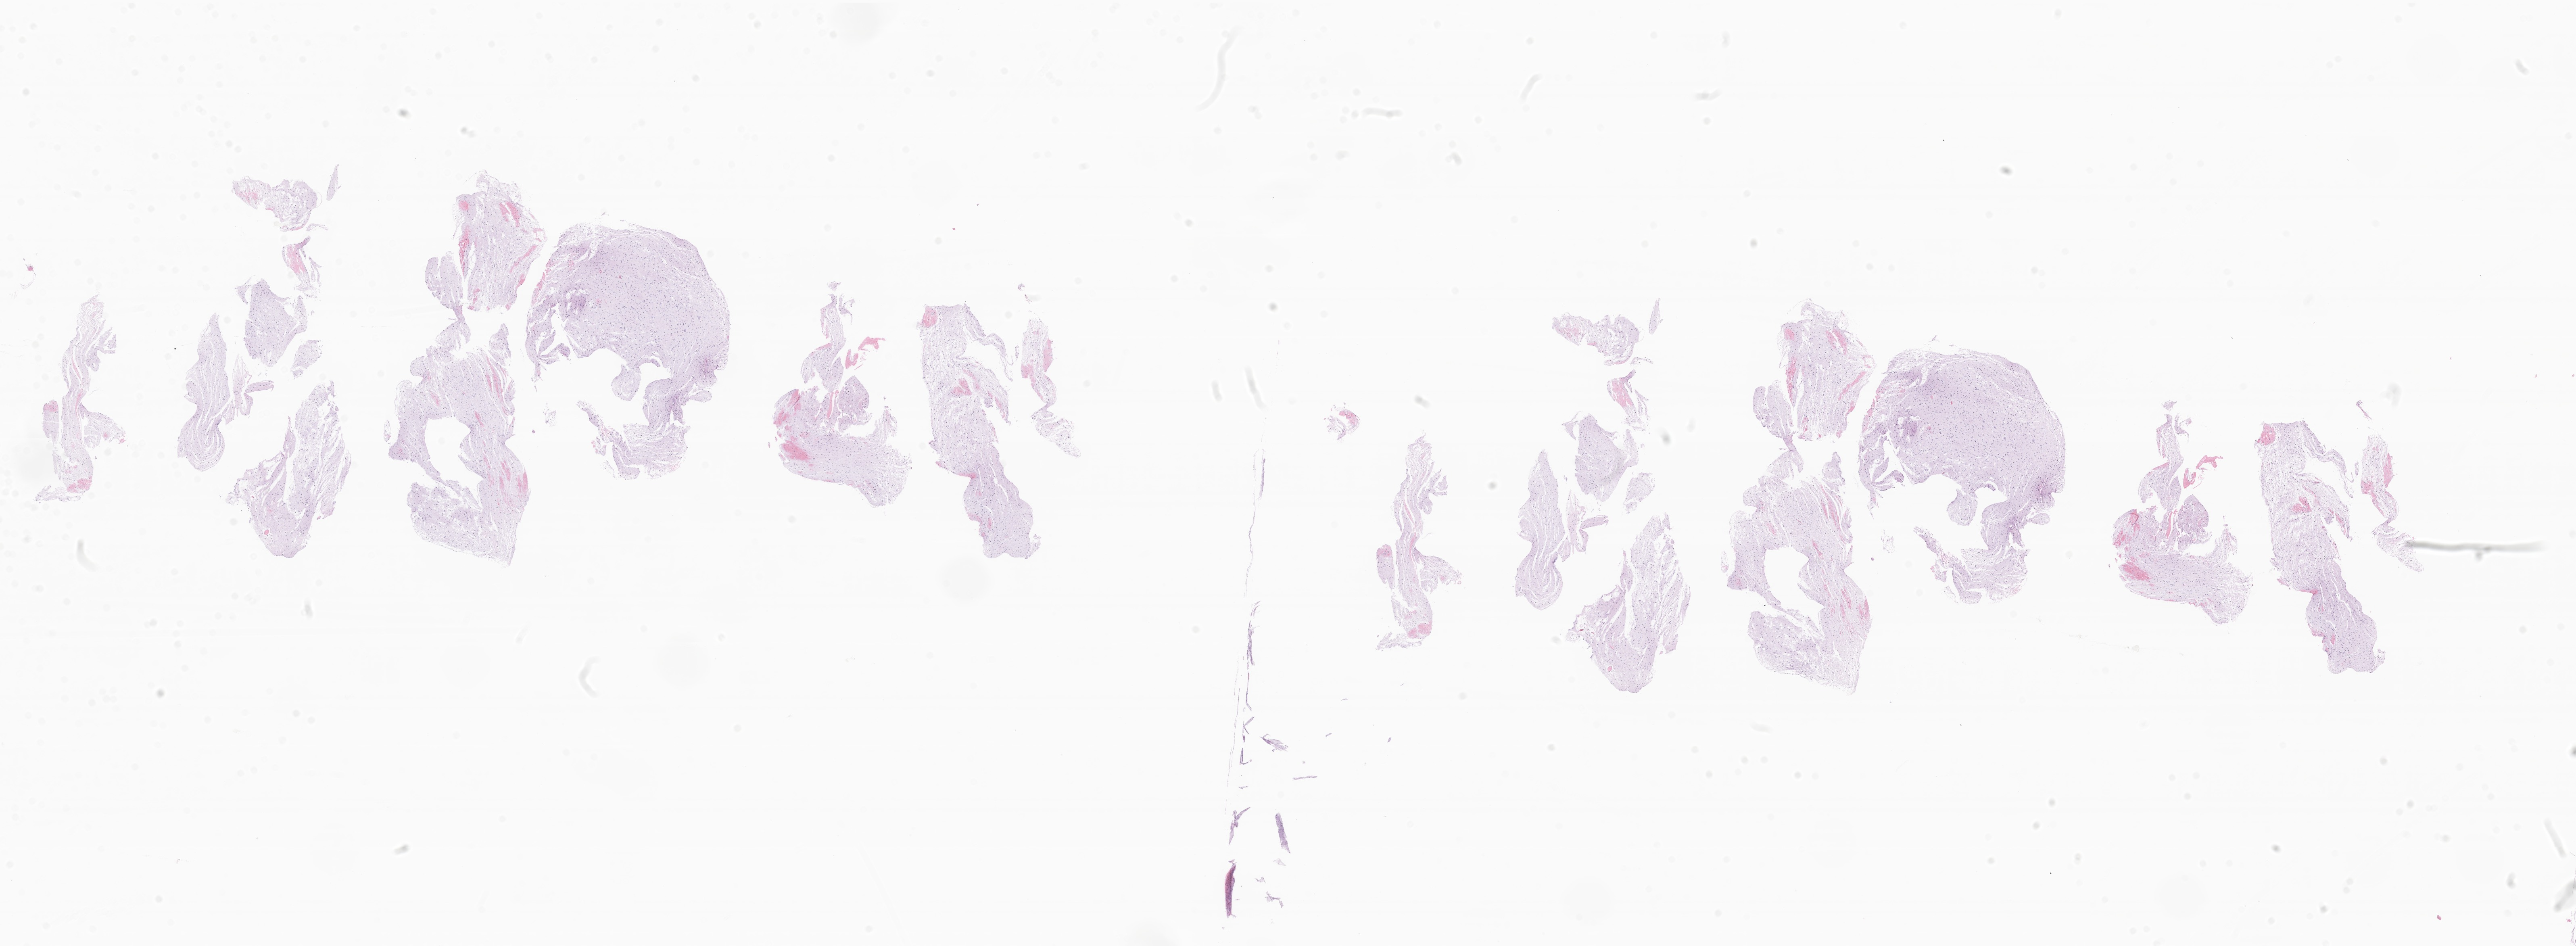
Haematoxylin and eosin whole-slide image of tumor tissue from the brain, a low-resolution overview of the entire scanned area, about 26.9 x 9.9 mm, formalin-fixed, paraffin-embedded (FFPE) tissue. Patient male; age 53 months (4 years 5 months).
Diagnosis (ICD-O-3 morphology term): Astrocytoma, NOS.